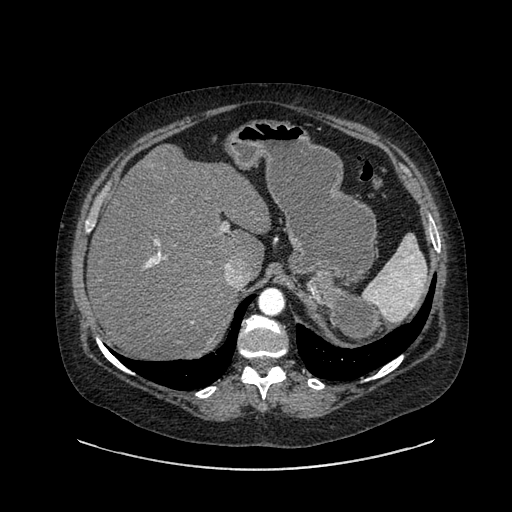
Contrast-enhanced abdominal CT, one axial slice; slice 631 of 769 in the series (ordered by position); reconstruction kernel SOFT; intravenous contrast given; soft-tissue window (W 400 / L 40 HU); 0.62 mm slice thickness; 512 × 512 image matrix. Female patient, age 61 years. Case-level facts recorded for this patient, not image findings: diagnosis: adrenocortical carcinoma; tumour side: left adrenal.
Annotated regions visible in this slice (semi-automatically segmented with operator editing):
- mass: box from (x=306, y=270) to (x=378, y=344) px